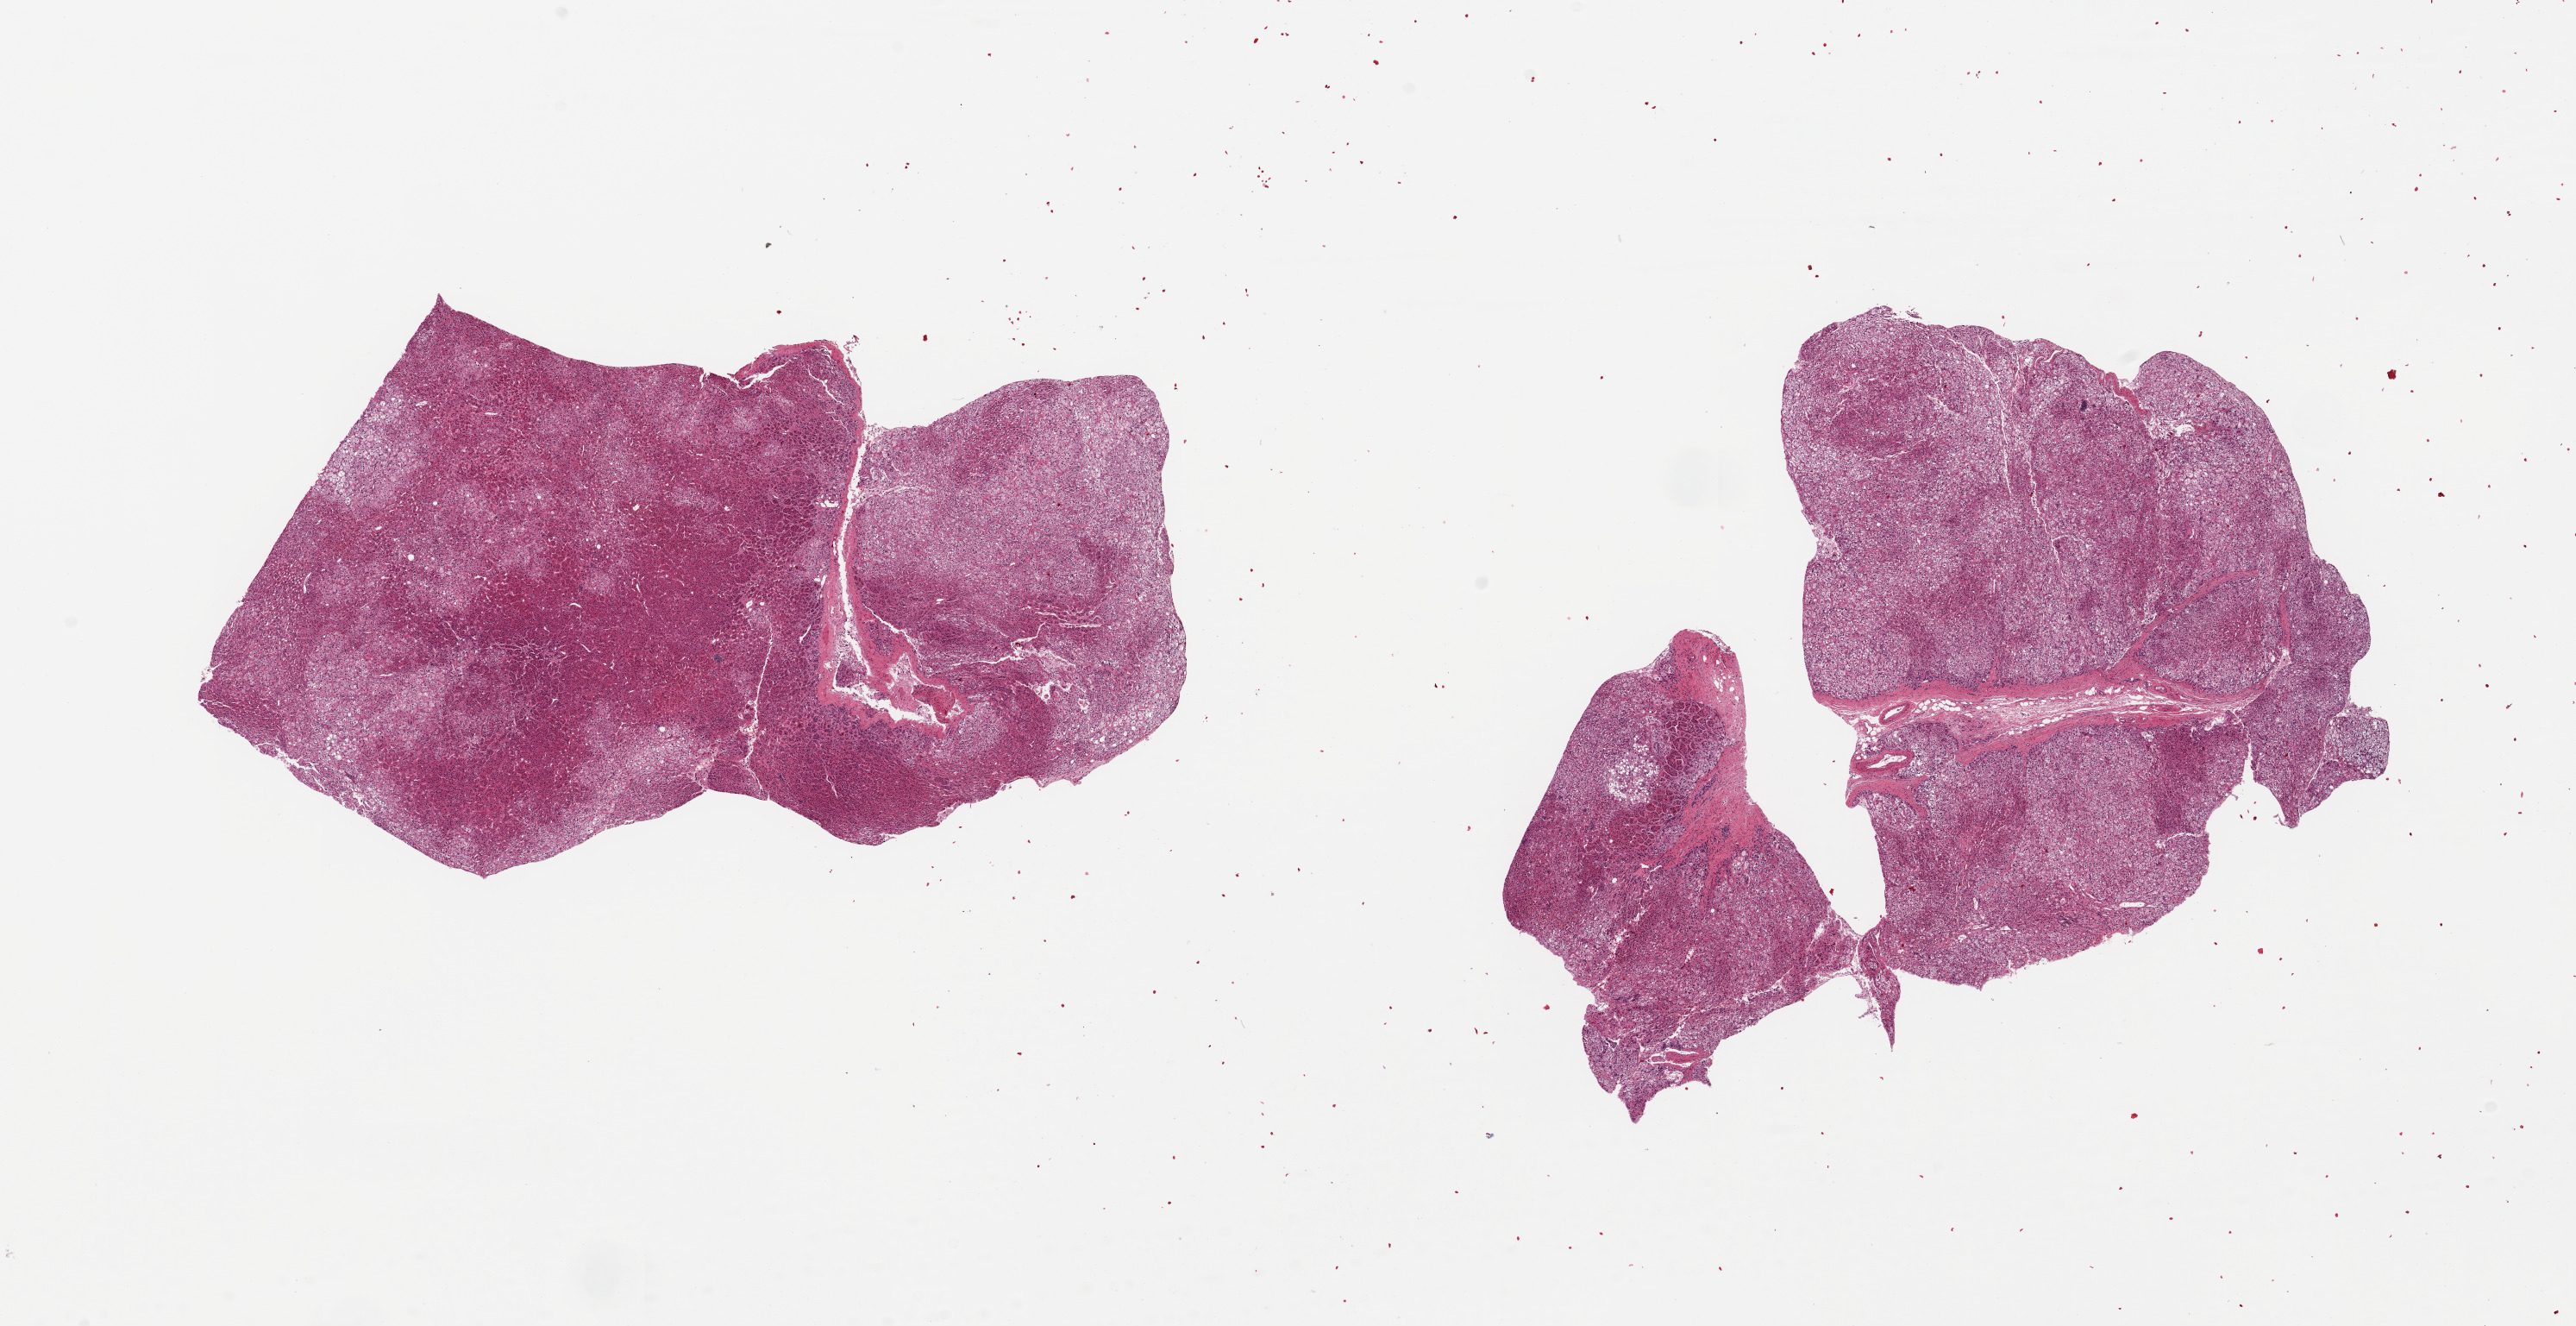
Digitized hematoxylin and eosin (H&E)-stained section, shown as a low-resolution overview of the whole scanned area (about 23.6 x 12.2 mm, from a 20x scan). PAXgene-fixed, paraffin-embedded tissue. Section of adrenal gland (target tissue). Donor tissue sample. Male donor.
Pathologist's review note for this sample: 2 pieces, all cortex.